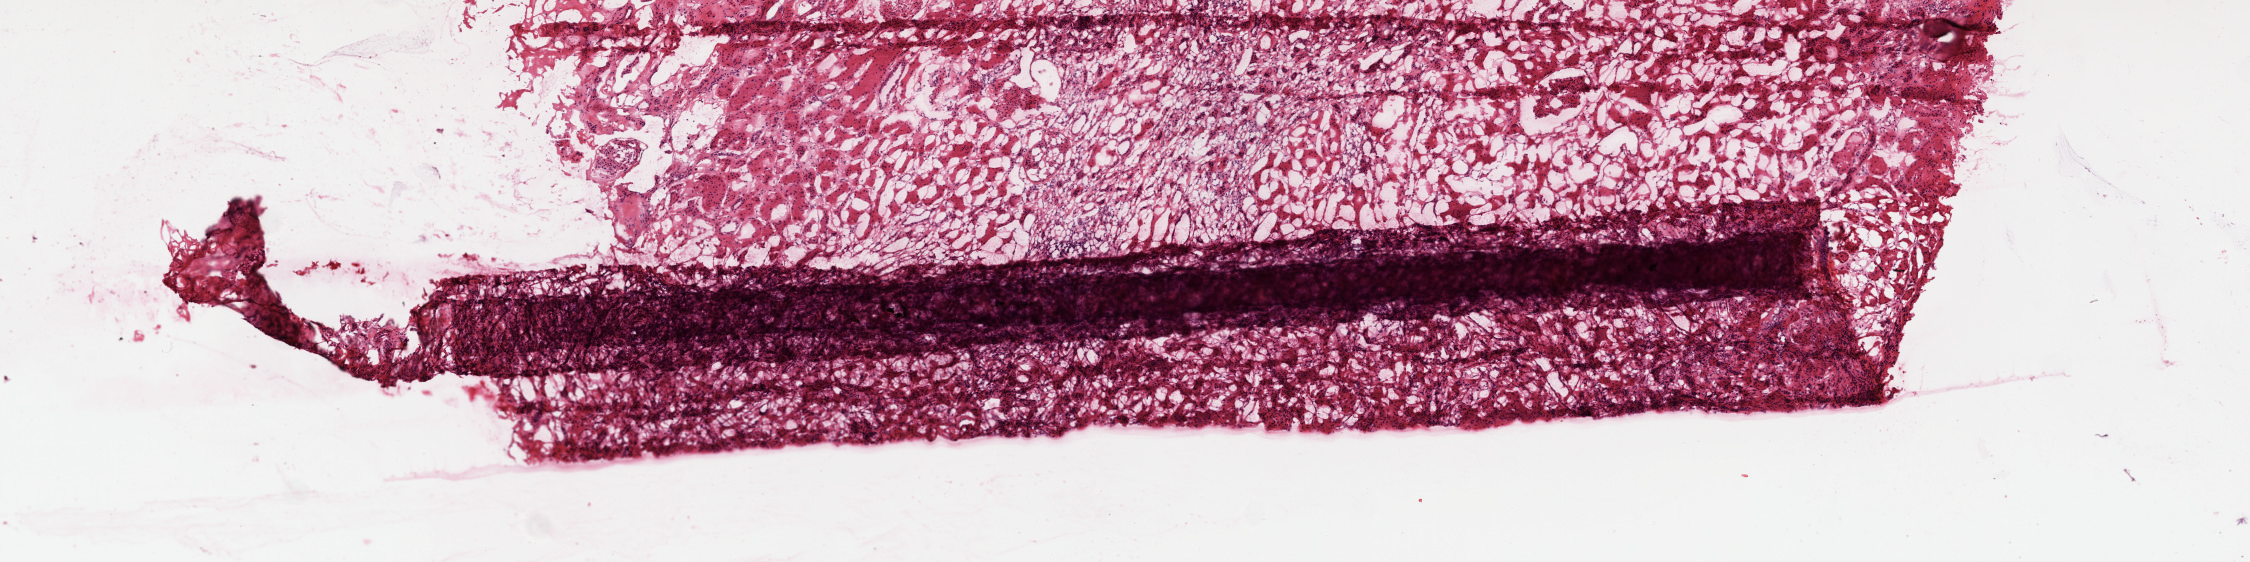
Whole-slide histology image, H&E — whole scanned area (about 9.0 x 2.3 mm, acquisition: 20x scan) shown as a low-resolution overview; frozen section; solid tissue normal (non-tumour tissue) sample from the kidney. Male, age 53 years at initial diagnosis.
- this section: solid tissue normal (non-tumour) sample from the same patient
- patient diagnosis: Clear cell adenocarcinoma, NOS